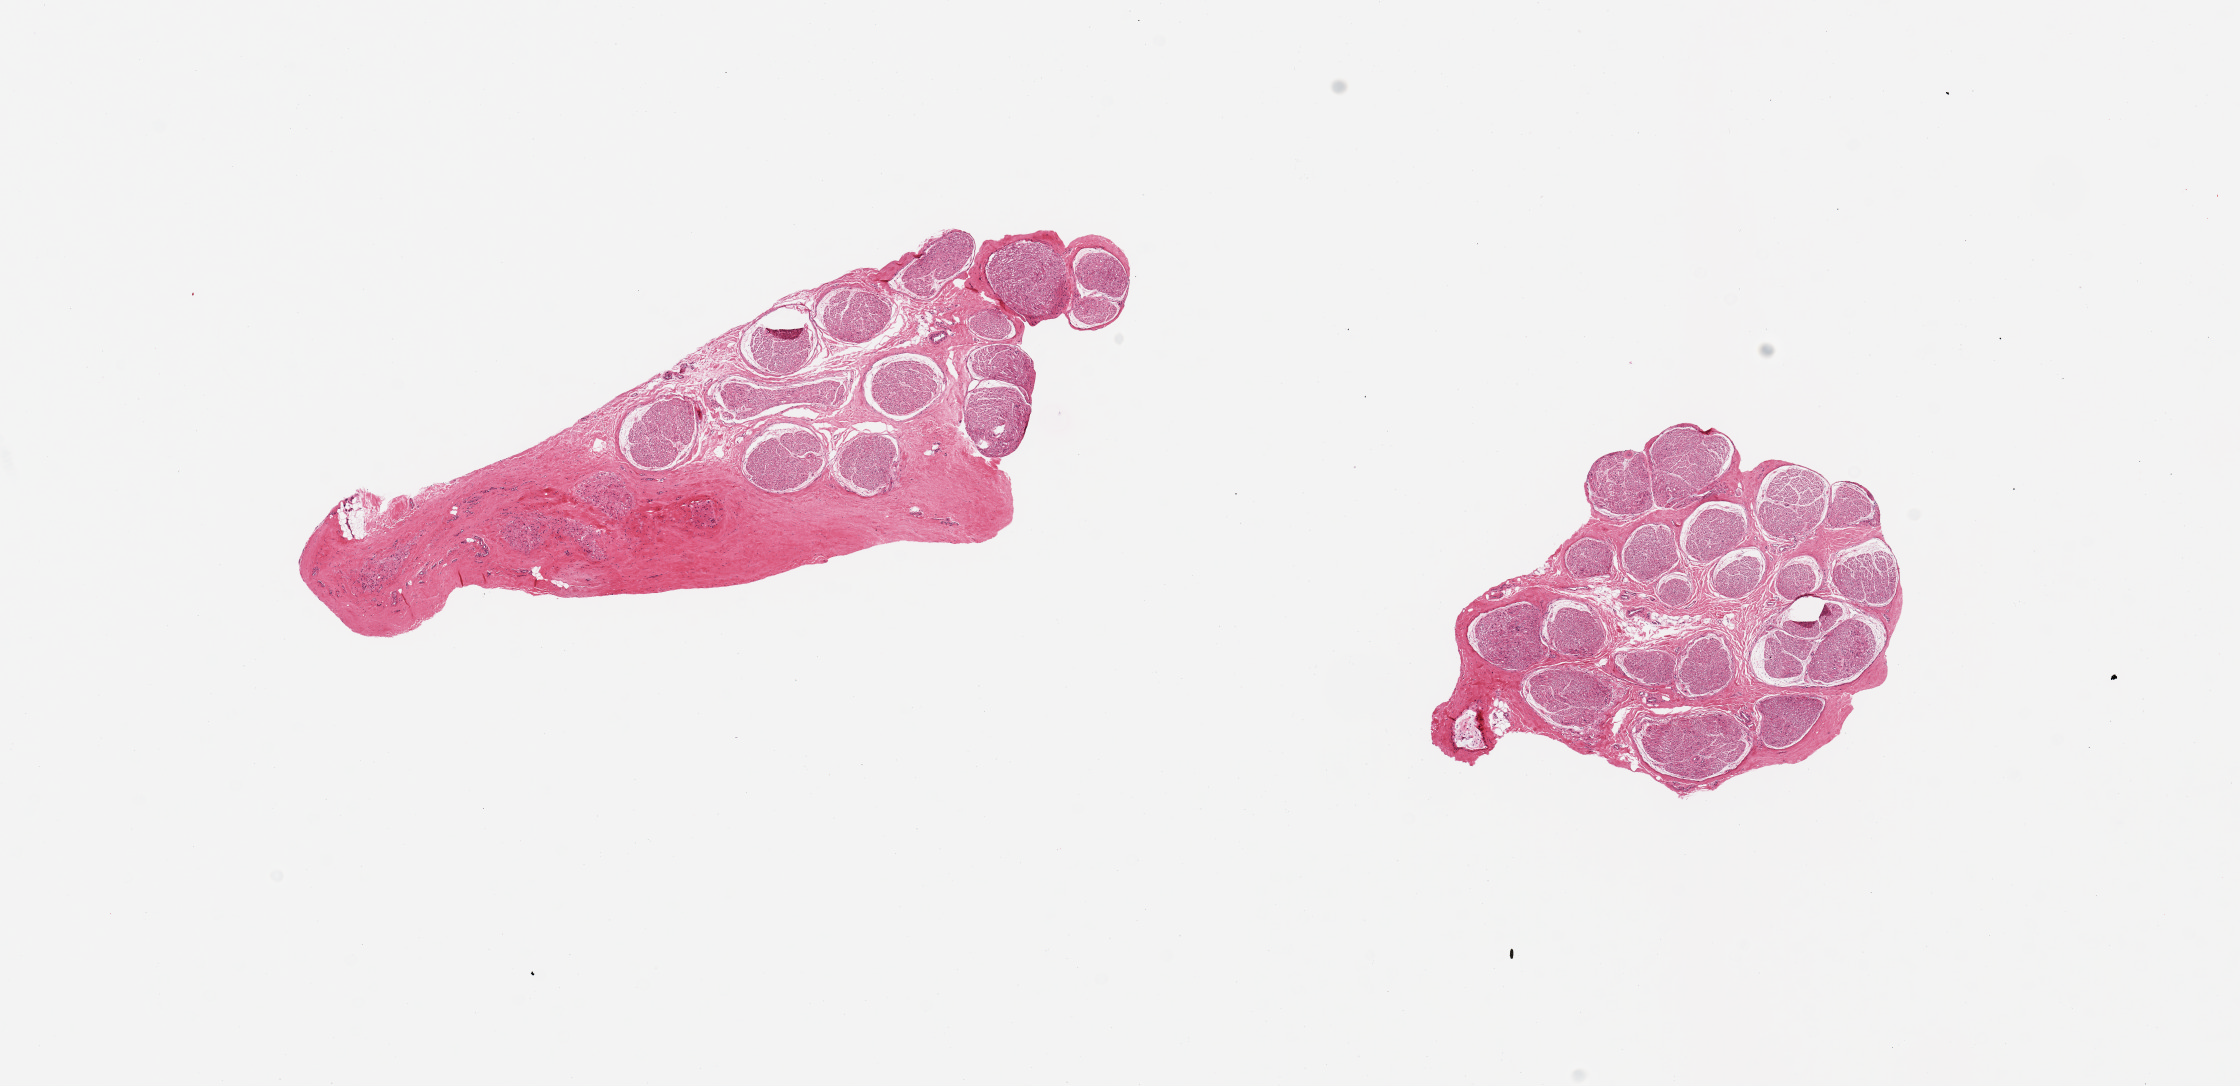
Digitized haematoxylin and eosin-stained section — whole scanned area (about 17.7 x 8.6 mm) shown as a low-resolution overview. PAXgene-fixed, paraffin-embedded tissue. Section of tibial nerve (target tissue). Donor tissue sample.
Reviewer comment on this tissue sample: 2 pieces, 7x2 & 4x3mm; 30% fibrous stroma in one.